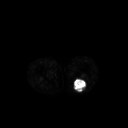
FDG PET of an extremity soft-tissue mass (from a PET/CT study), one axial slice; 3.27 mm slice thickness; 128 × 128 image matrix, field of view 500 × 500 mm. Patient: male, 54 years. Case-level facts recorded for this patient, not image findings: histological type: synovial sarcoma; site of the primary tumour: left poplietal fossa.
Outlined on this slice (expert contour drawn on MRI and transferred to this co-registered scan by the dataset authors):
- gross tumour volume (mass): bounding box (x1, y1, x2, y2) in pixels: (73, 79, 88, 92)